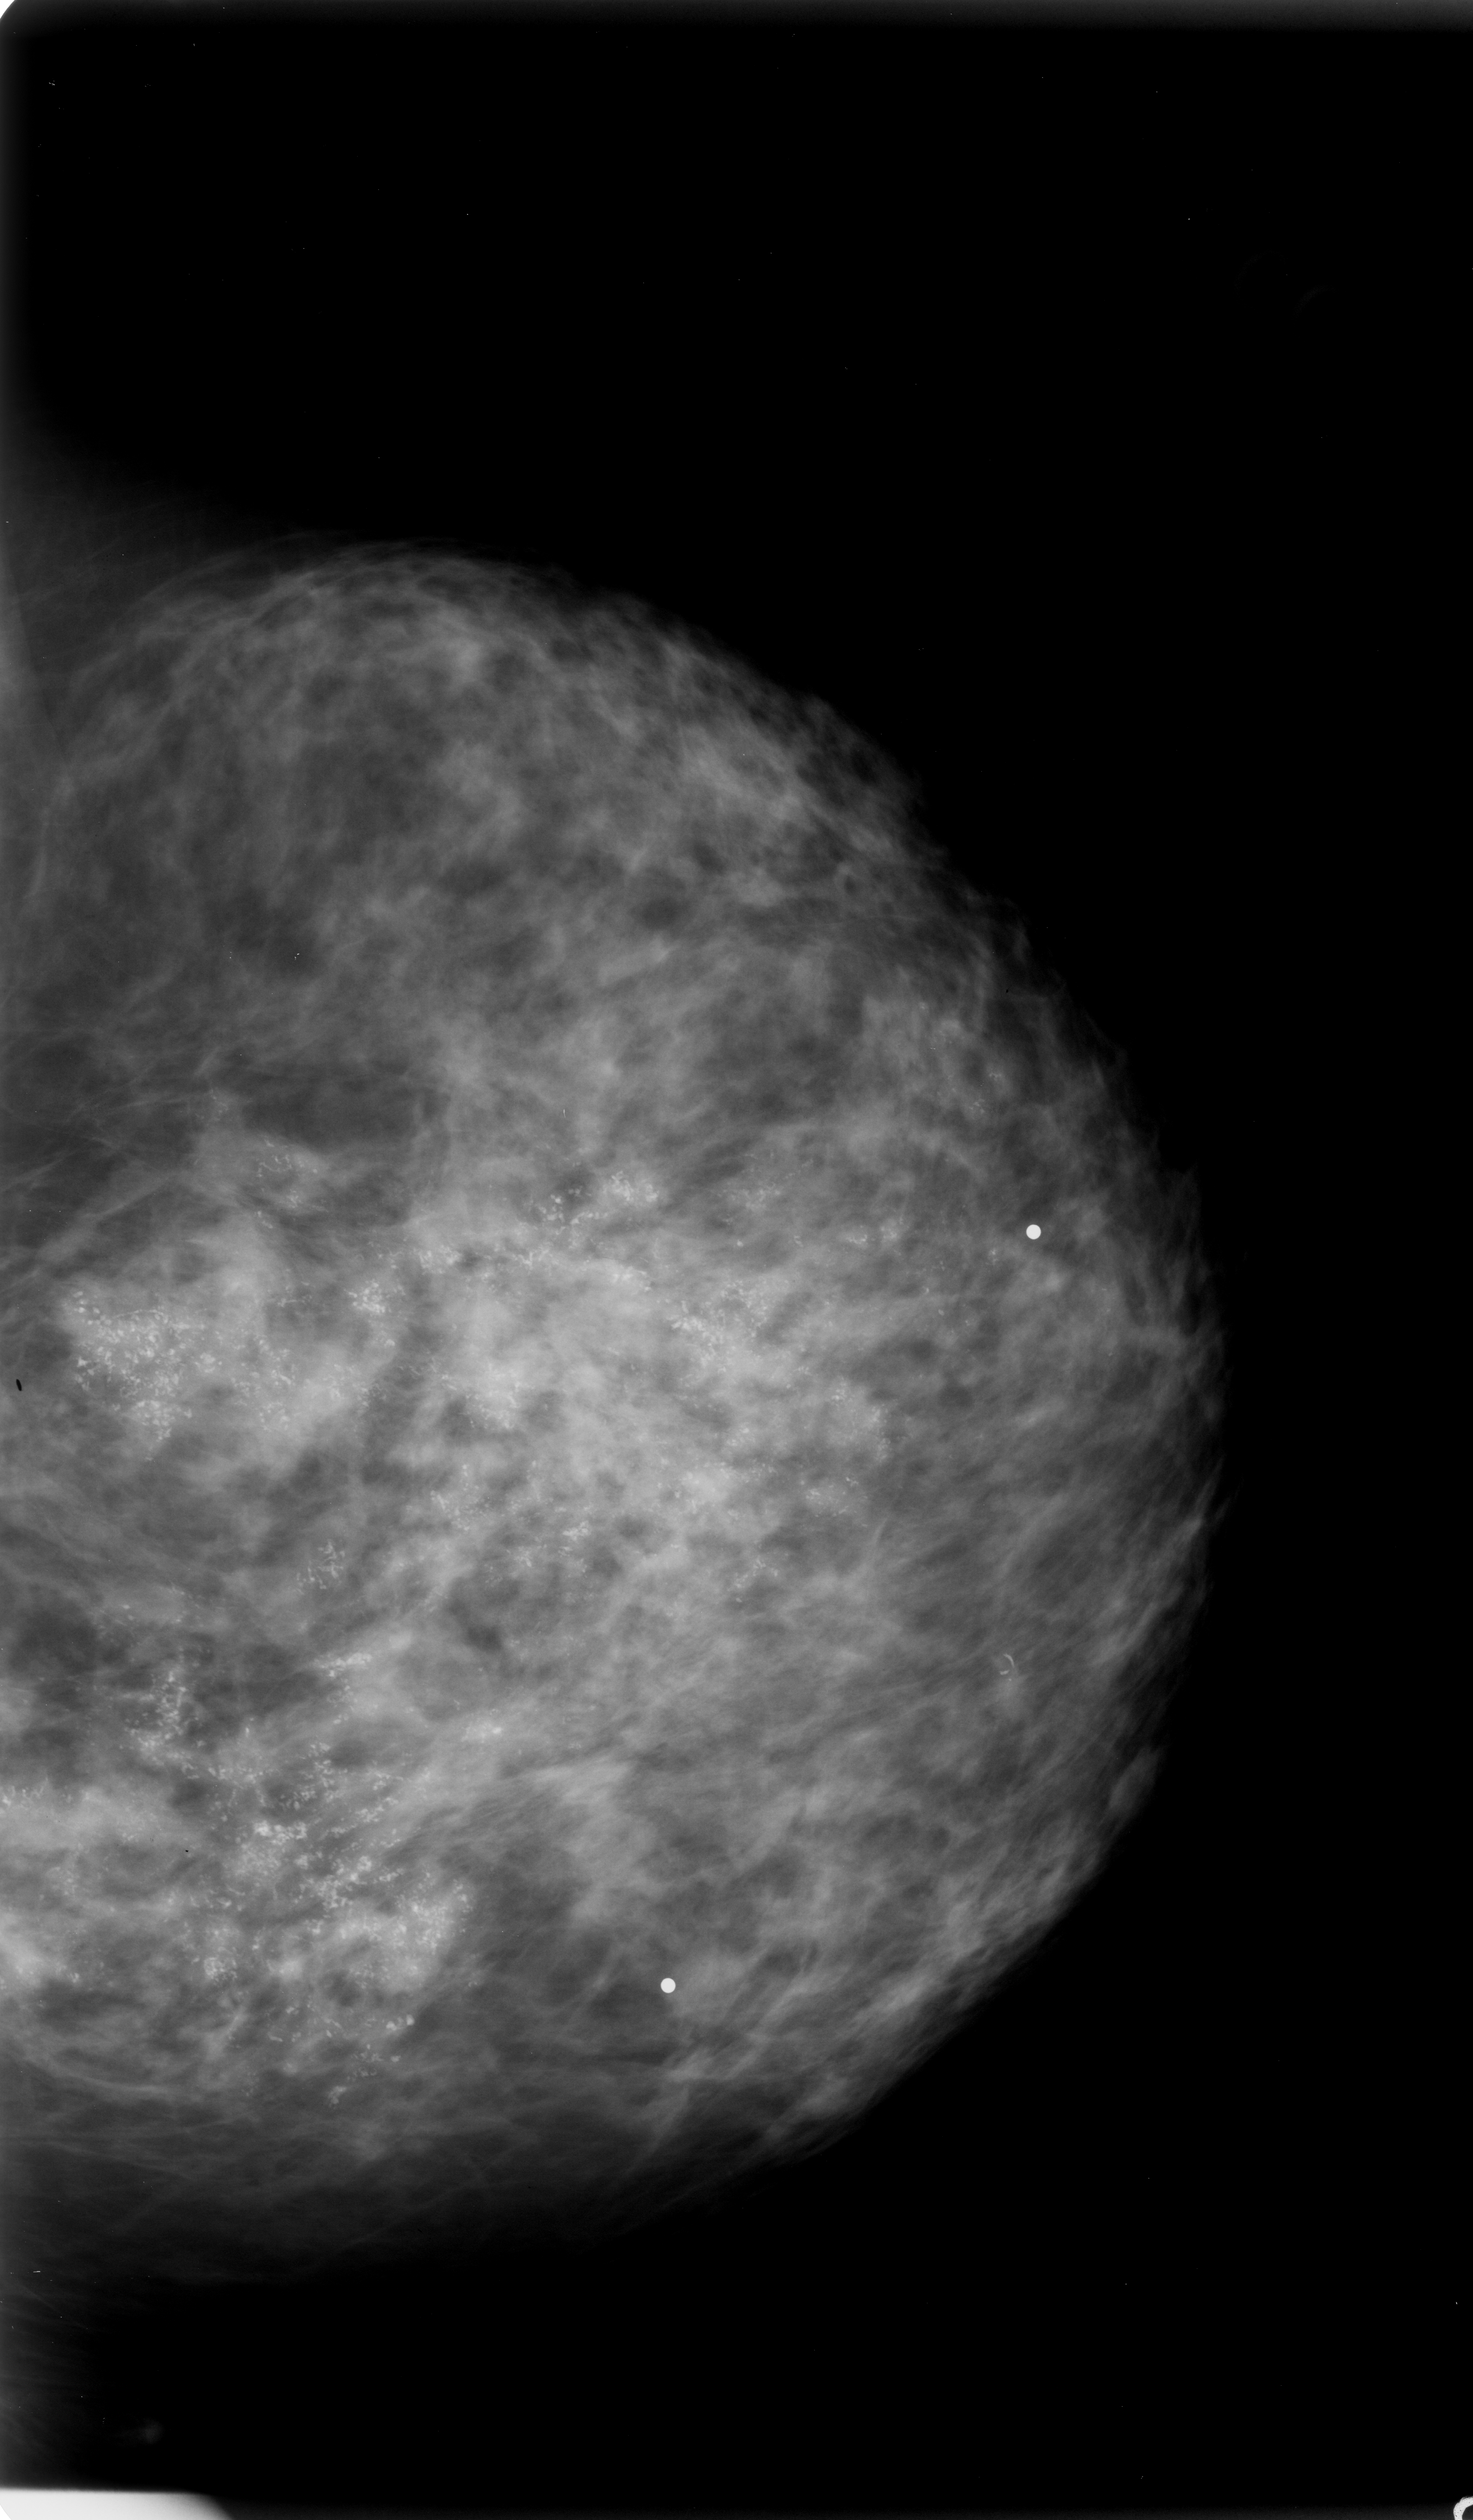
Mammogram (digitized film), left breast, CC view, breast composition: heterogeneously dense (BI-RADS density category 3 of 4).
- Radiologist-marked abnormalities on this image: calcifications, morphology pleomorphic, distribution regional; BI-RADS assessment category 5; subtlety rating 5 on a 1 (subtle) to 5 (obvious) scale; pathology result (as recorded, not read from the image): malignant.